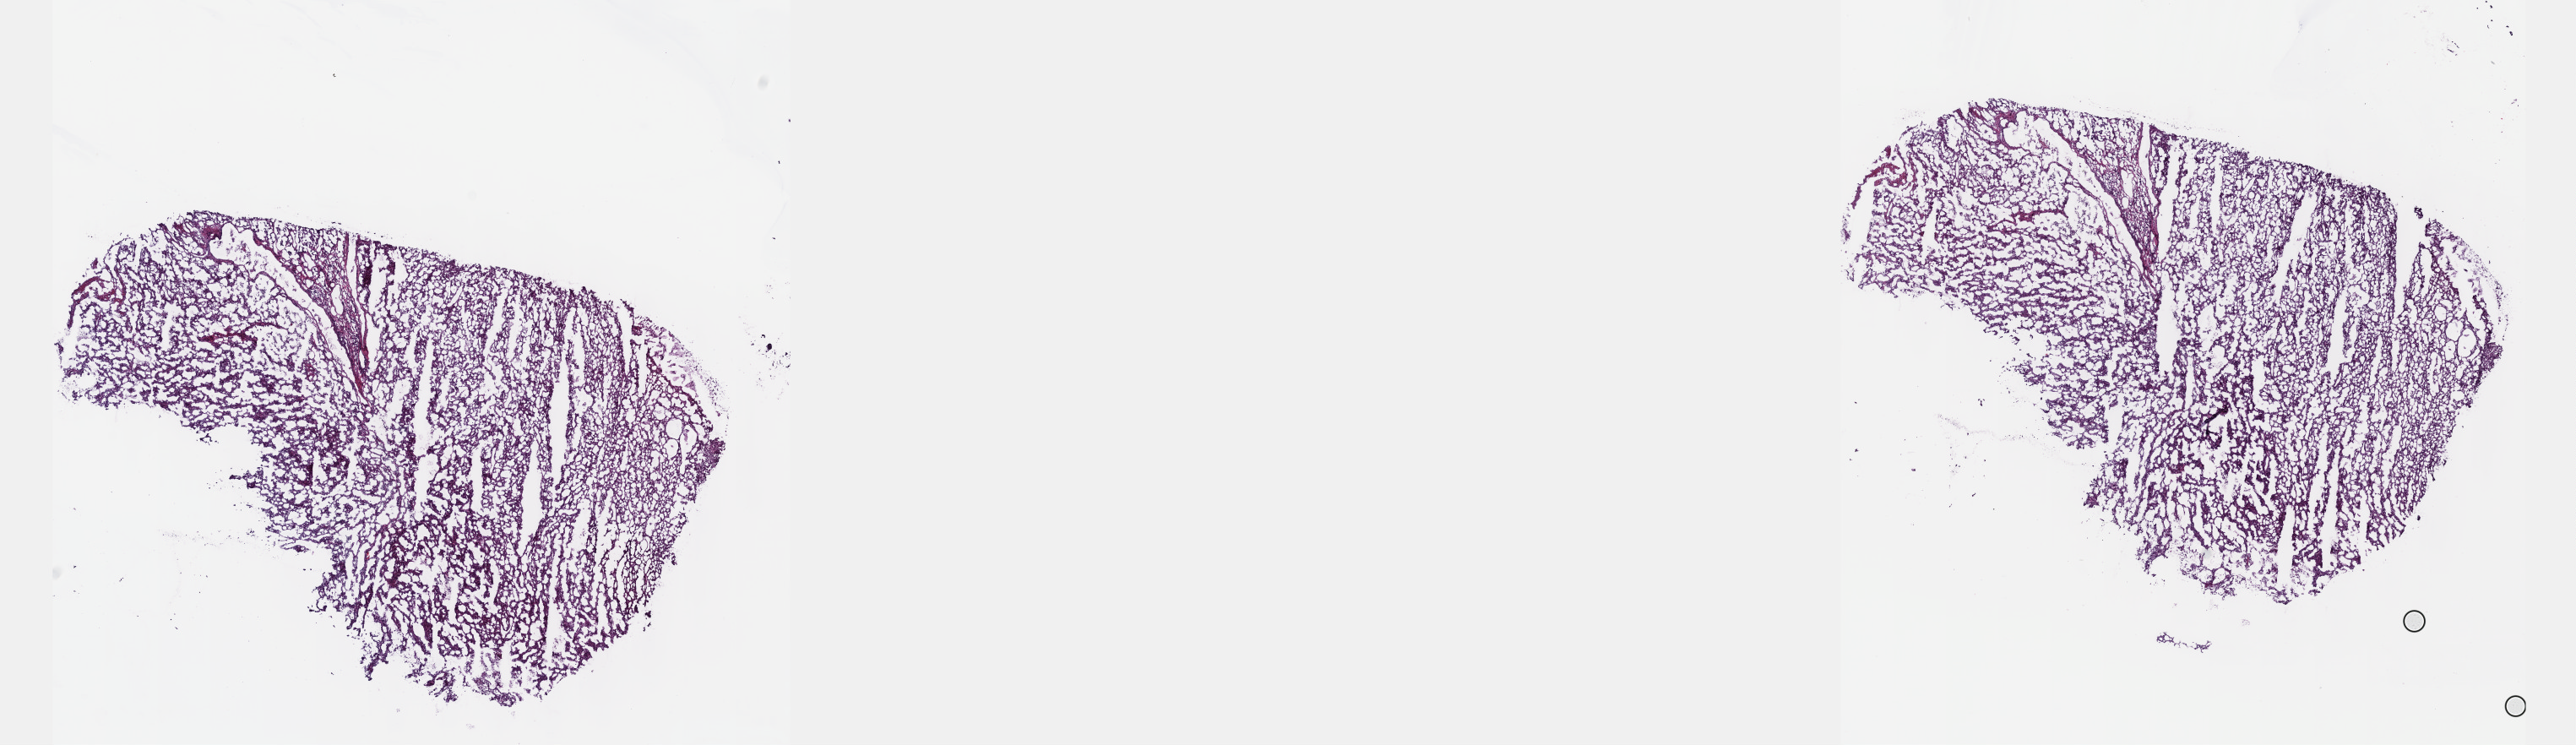
Hematoxylin and eosin (H&E) stained whole-slide image, low-resolution overview of the scanned area, about 24.6 x 7.1 mm; frozen section from the top of the tissue portion; primary tumour sample from the kidney. Patient: female, age at initial diagnosis 81 years. Histologic grade: G3 (poorly differentiated). Slide review estimates, as recorded: tumour cells 60%, tumour nuclei 85%, normal cells 0%, stromal cells 30%, necrosis 10%. Infiltration values recorded for this section: lymphocyte infiltration 10%, monocyte infiltration 0%, neutrophil infiltration 0%.
Lymph nodes positive (case pathology): 0 of 2 examined. AJCC pathologic stage: I (6th edition). Diagnosis: Clear cell adenocarcinoma, NOS. TNM: T1b N0 MX.